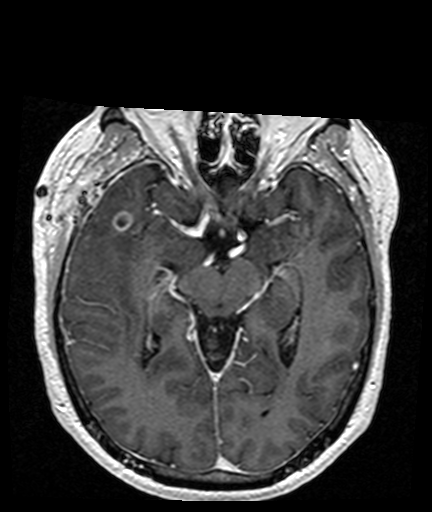
Brain MRI from a brain-tumour surgery series, one axial slice; position 99 of 176 along the scan axis; T1-weighted post-contrast; 1 mm slice thickness; 432 × 512 image matrix, field of view 194 × 230 mm. Case-level facts recorded for this patient, not image findings: histopathology: Glioblastoma; WHO grade: 4; IDH mutation: no; tumour location: Right Frontal Temporal, Posterior Sylvian Fissure.
Annotated regions visible in this slice (outlined manually by an expert reader):
- tumour: bounding box (x1, y1, x2, y2) in pixels: (112, 213, 133, 232)